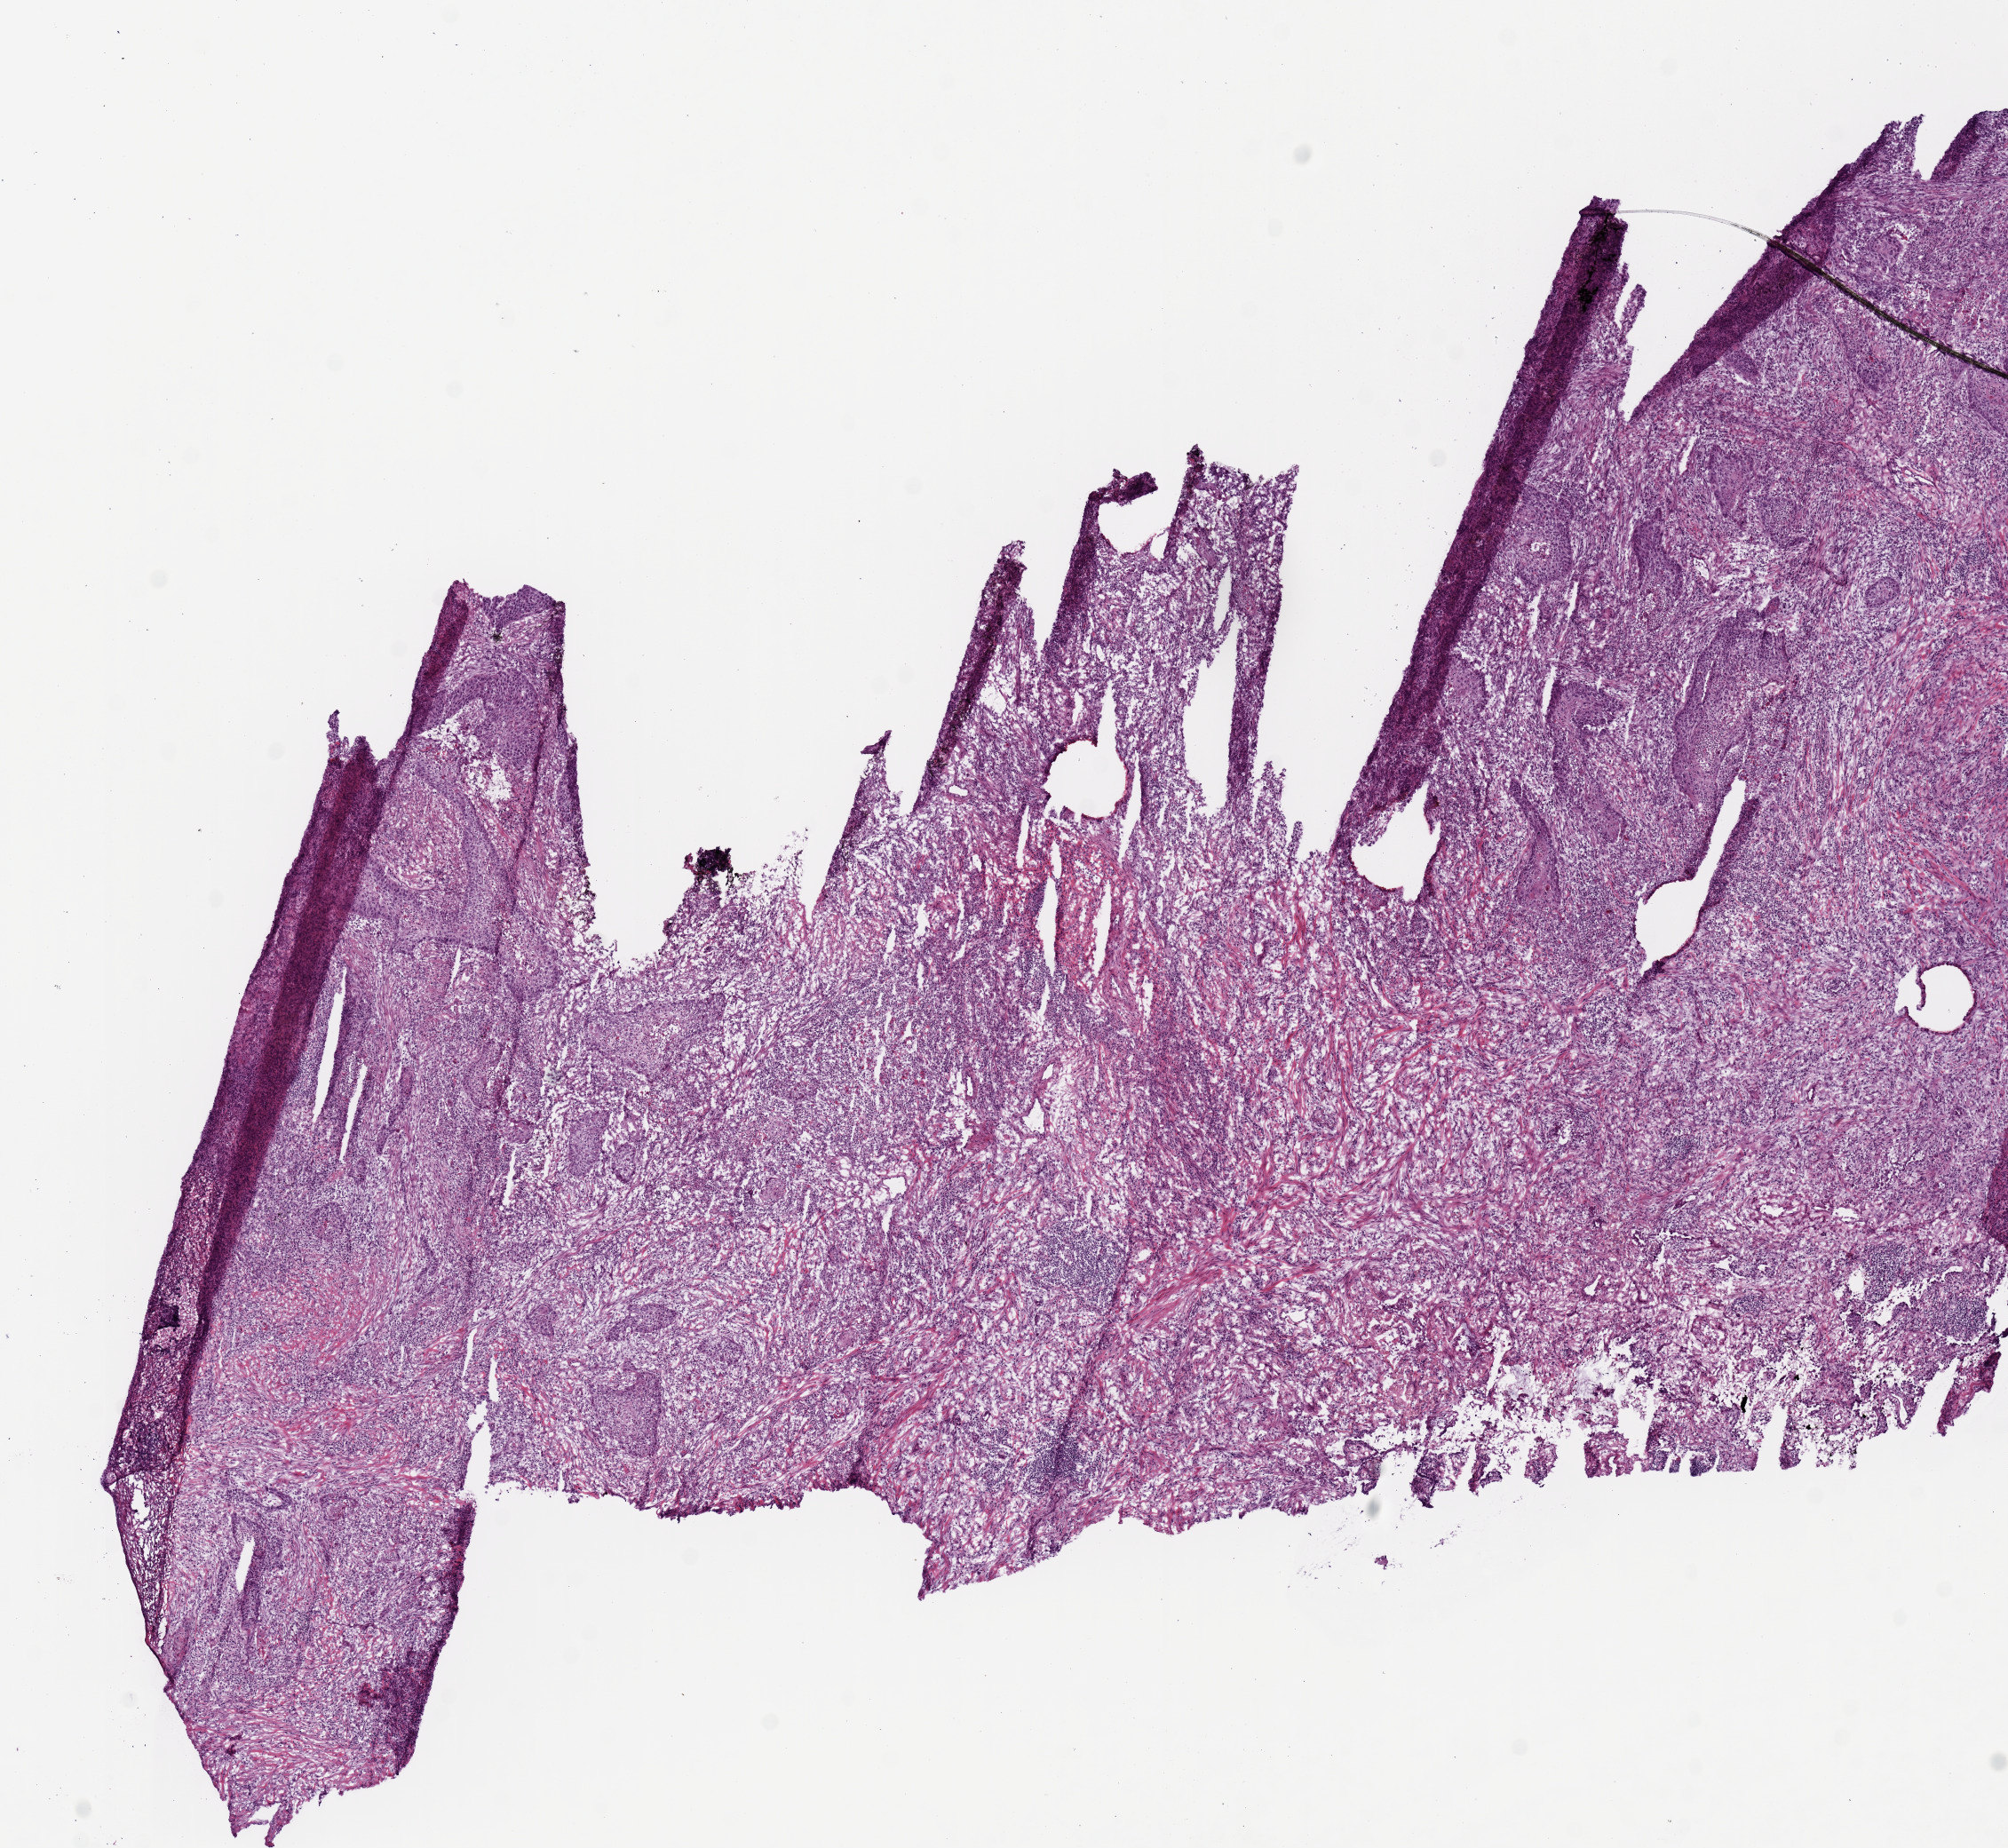
H&E whole-slide image — shown as a low-resolution overview of the whole scanned area (about 9.0 x 8.3 mm, slide scanned at 20x), frozen section from the top of the tissue portion, primary tumour sample from the lung. Female, age 76 years at initial diagnosis. Pathologist review of this section (percent, as recorded): tumour cells 85%, tumour nuclei 60%, normal cells 0%, stromal cells 15%, necrosis 0%.
AJCC pathologic stage: IIB (7th edition). Pathologic diagnosis: Squamous cell carcinoma, NOS (lower lobe, lung). Laterality: right.